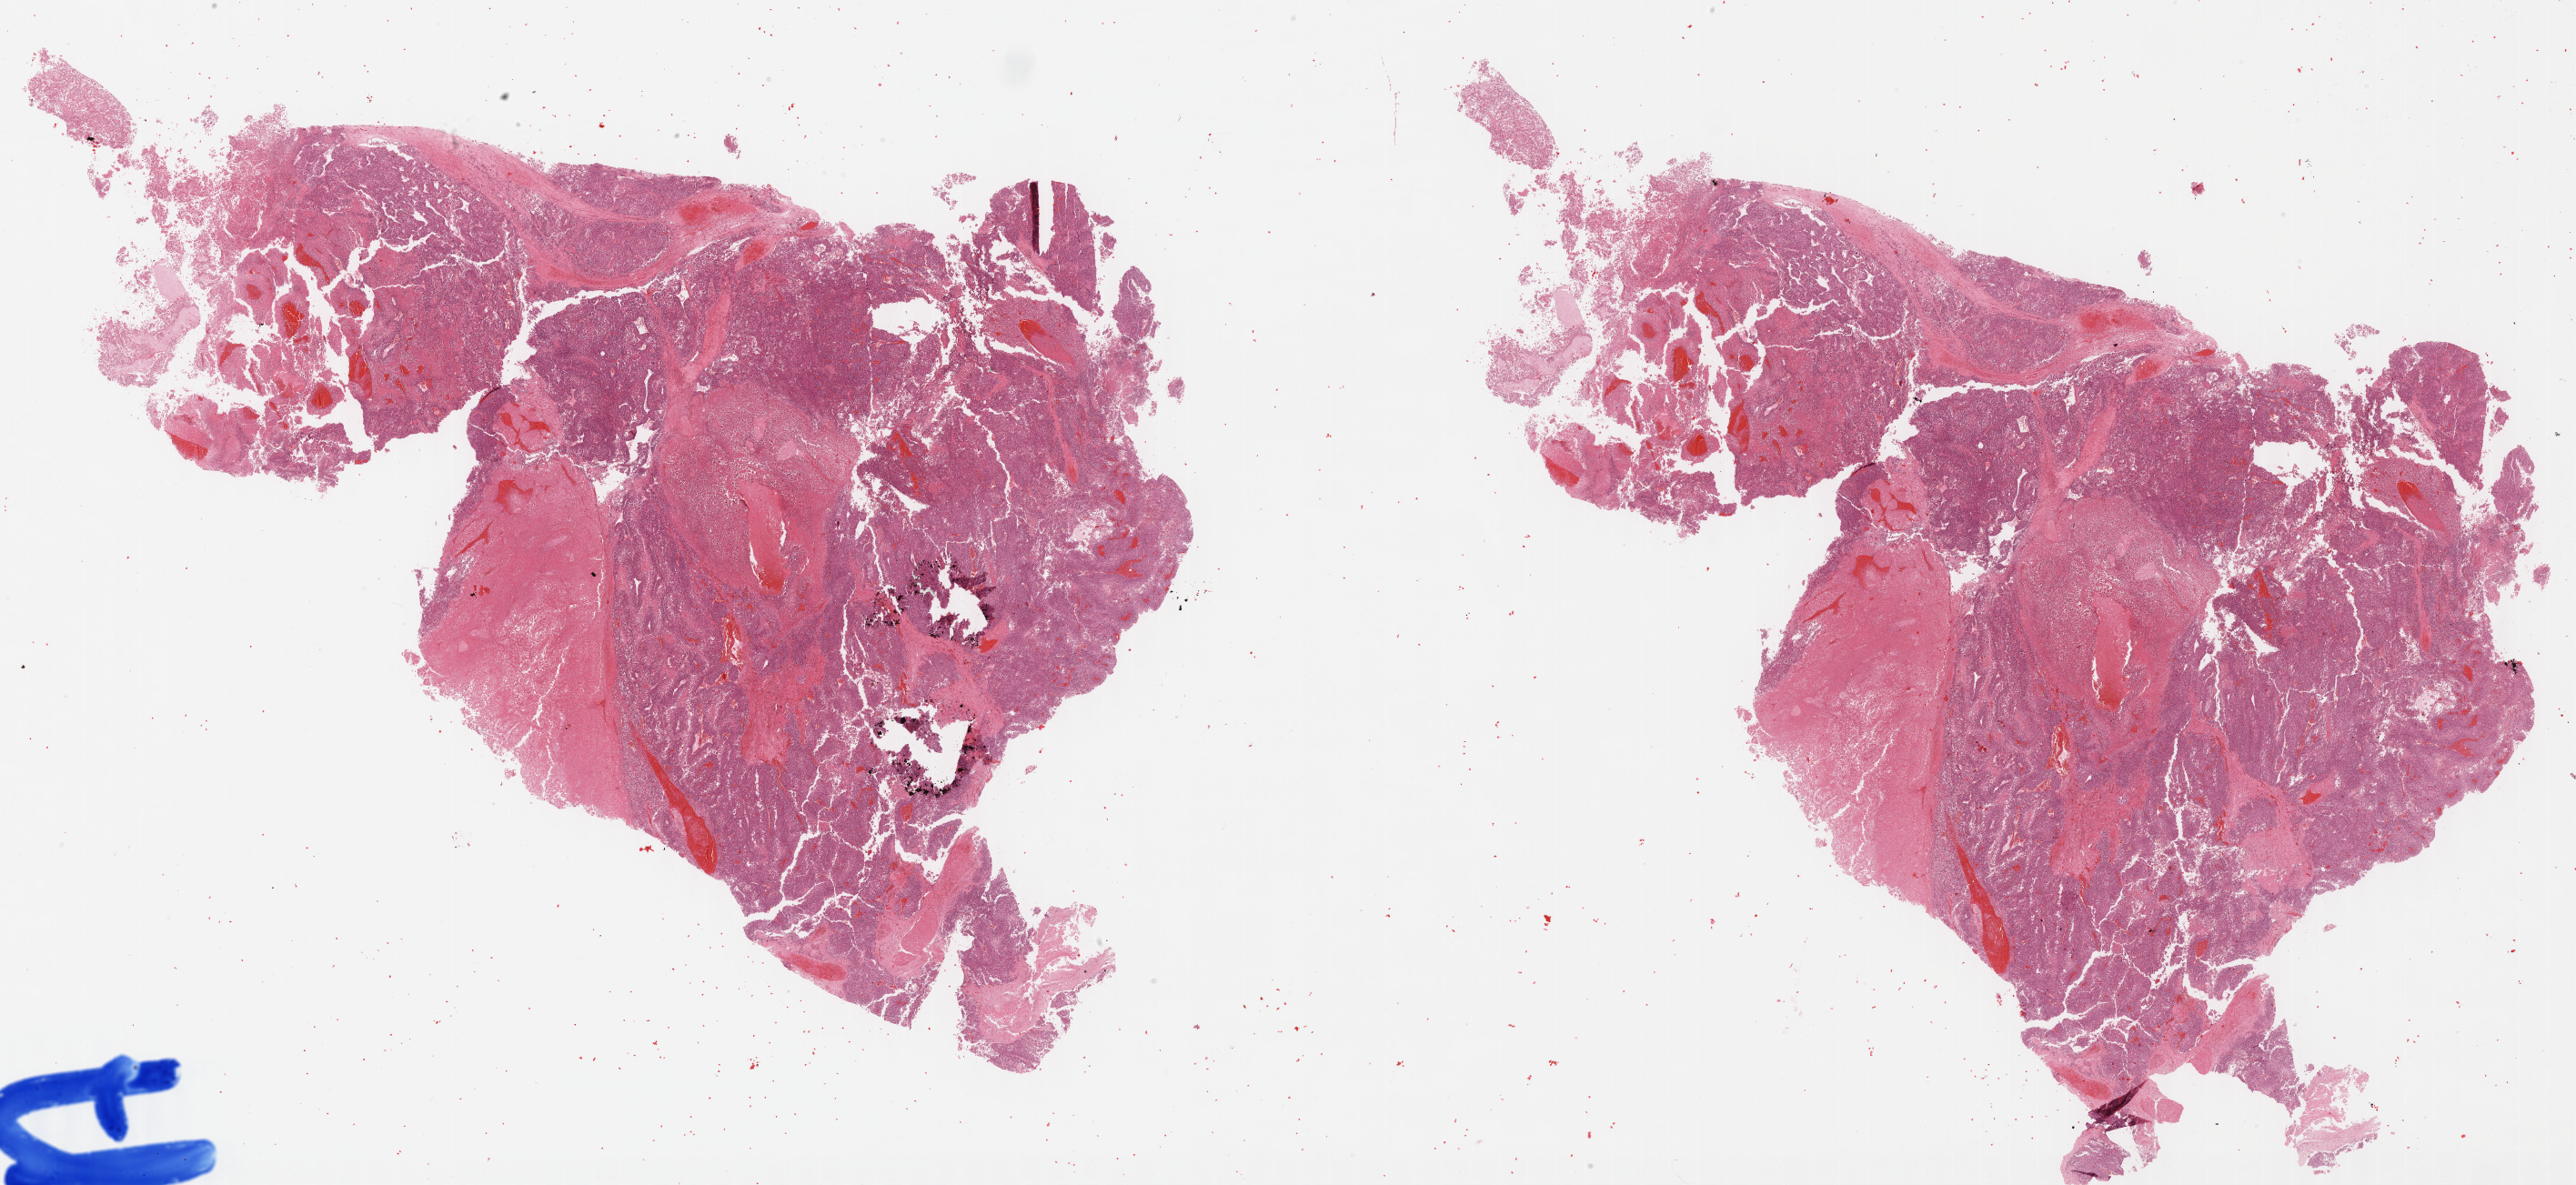
Whole-slide histology image, H&E, a low-resolution overview of the entire scanned area, about 45.8 x 21.1 mm (slide scanned at 40x). Formalin-fixed paraffin-embedded (FFPE) diagnostic section. Adrenal cortex, primary tumour sample. Patient: female, age at initial diagnosis 53 years.
* histologic diagnosis: Adrenal cortical carcinoma (cortex of adrenal gland)